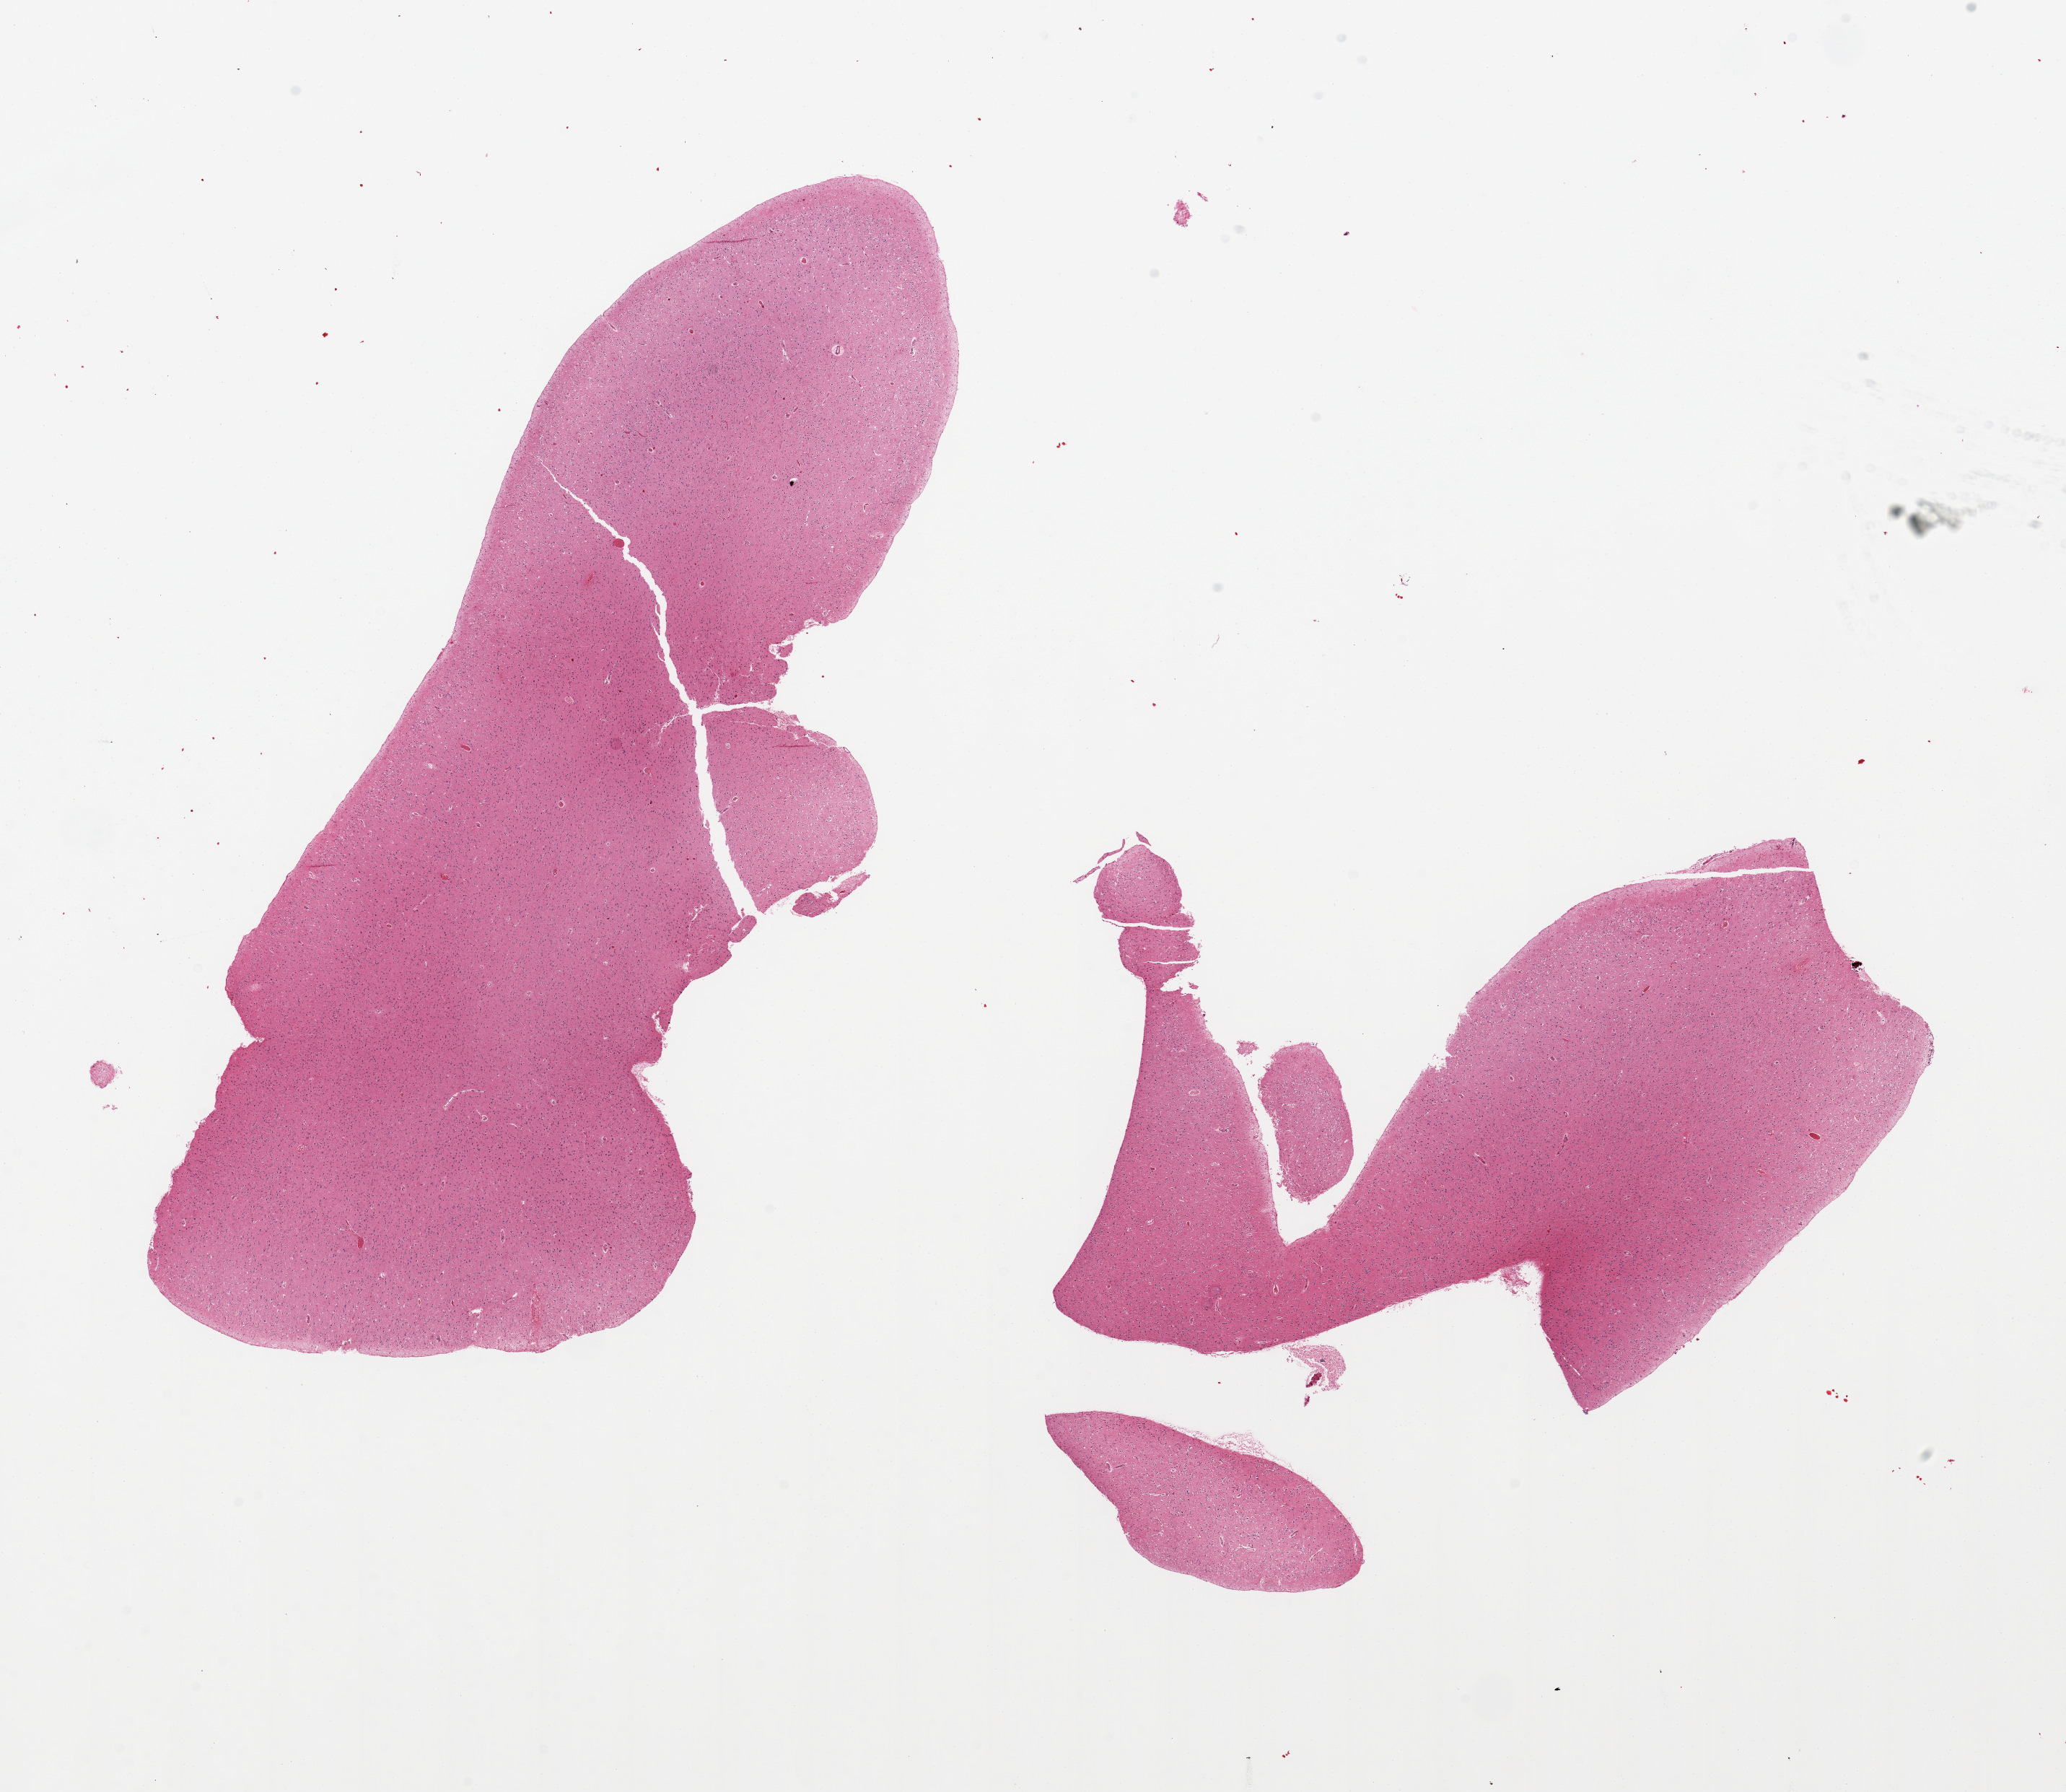
Whole-slide image, H&E stain — low-resolution overview of the scanned area, about 22.6 x 19.6 mm. PAXgene-fixed paraffin-embedded (PFPE) section. Target tissue: cerebral cortex. Donor tissue sample. Female donor.
* pathologist's review note for this sample: 2 pieces, no abnormalities